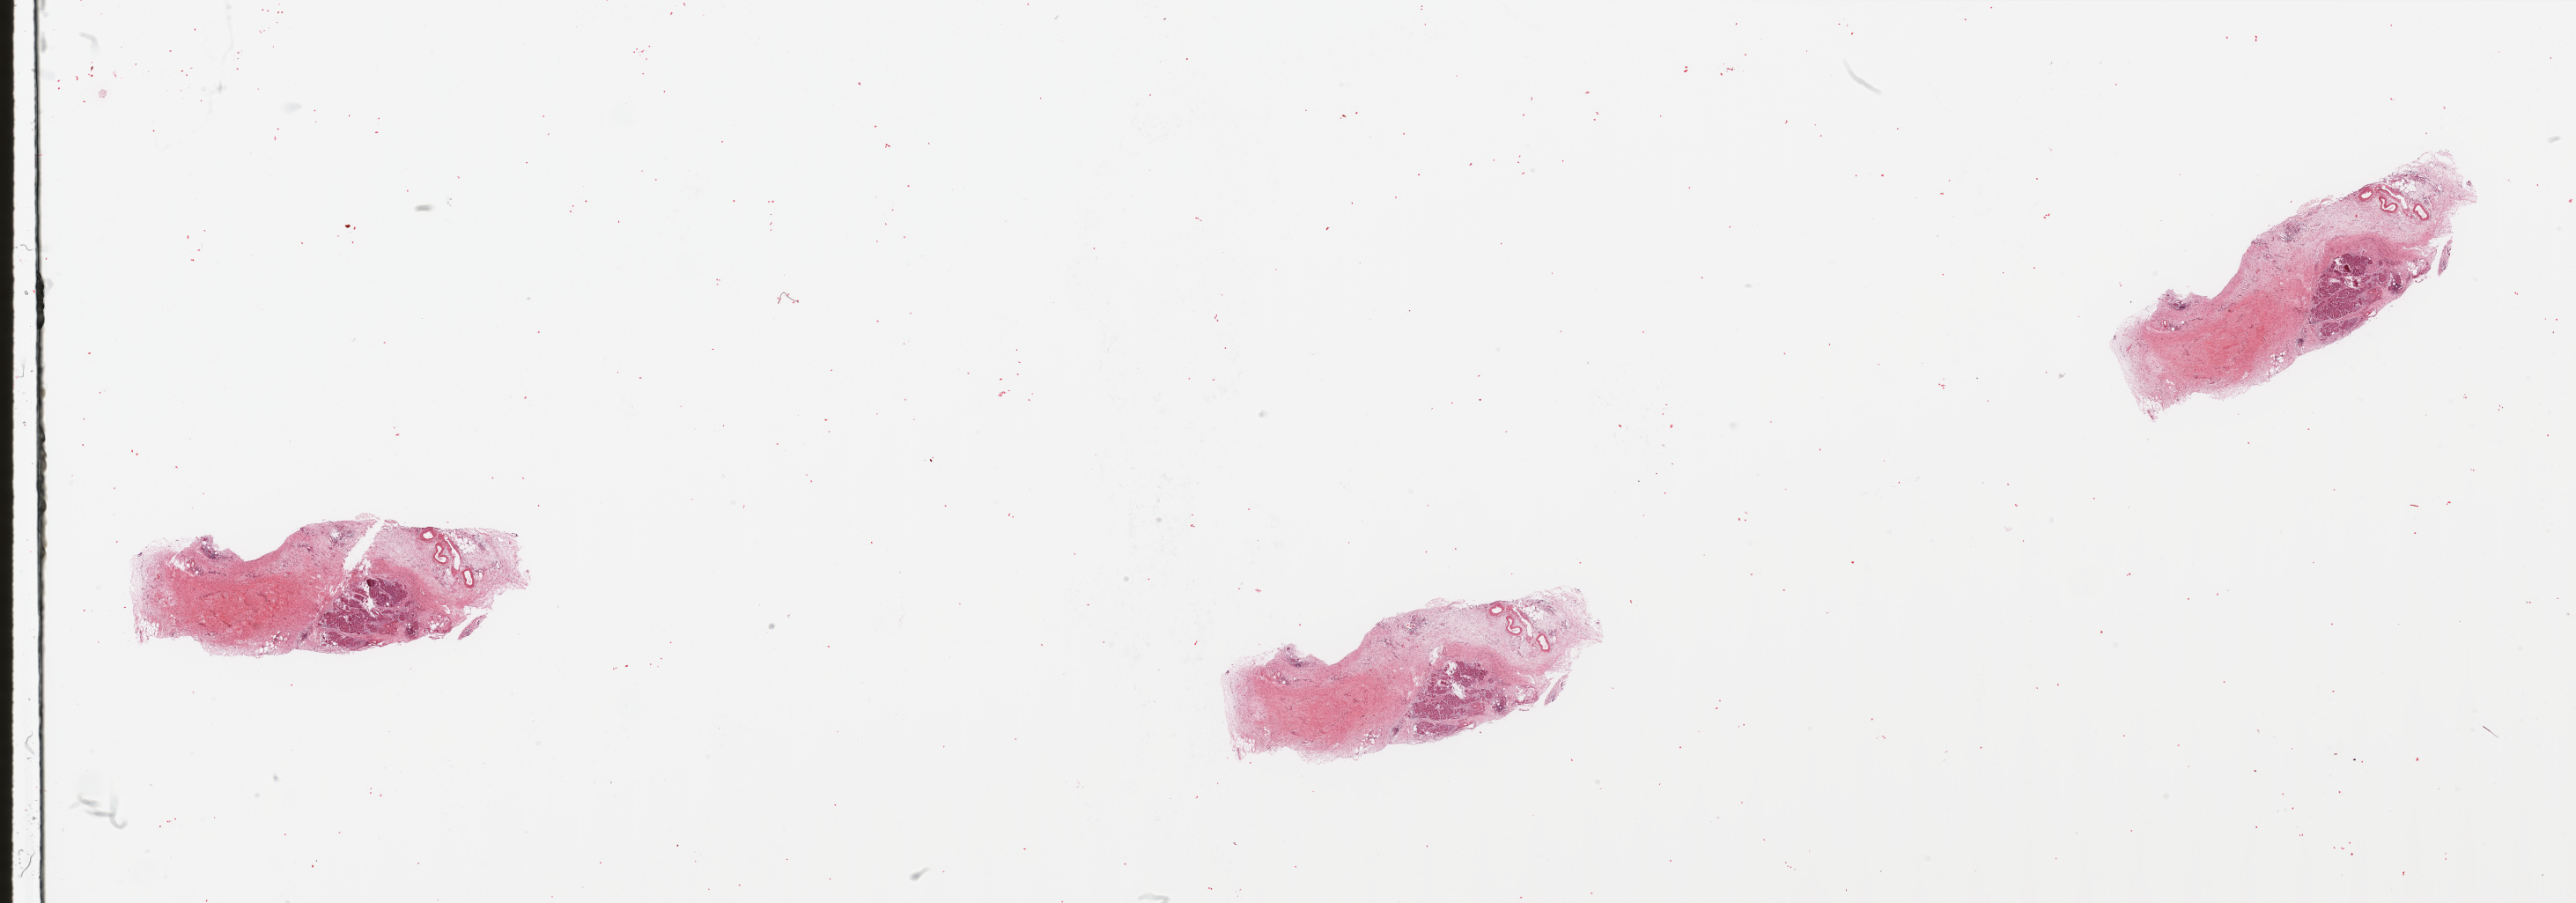
Hematoxylin and eosin (H&E) stained whole-slide image — a low-resolution overview of the entire scanned area, about 46.3 x 16.2 mm; pancreas, normal (non-tumour) tissue. Patient: female, age 68 years.
• this section: normal (non-tumour) tissue from the same patient
• patient diagnosis: Infiltrating duct carcinoma, NOS